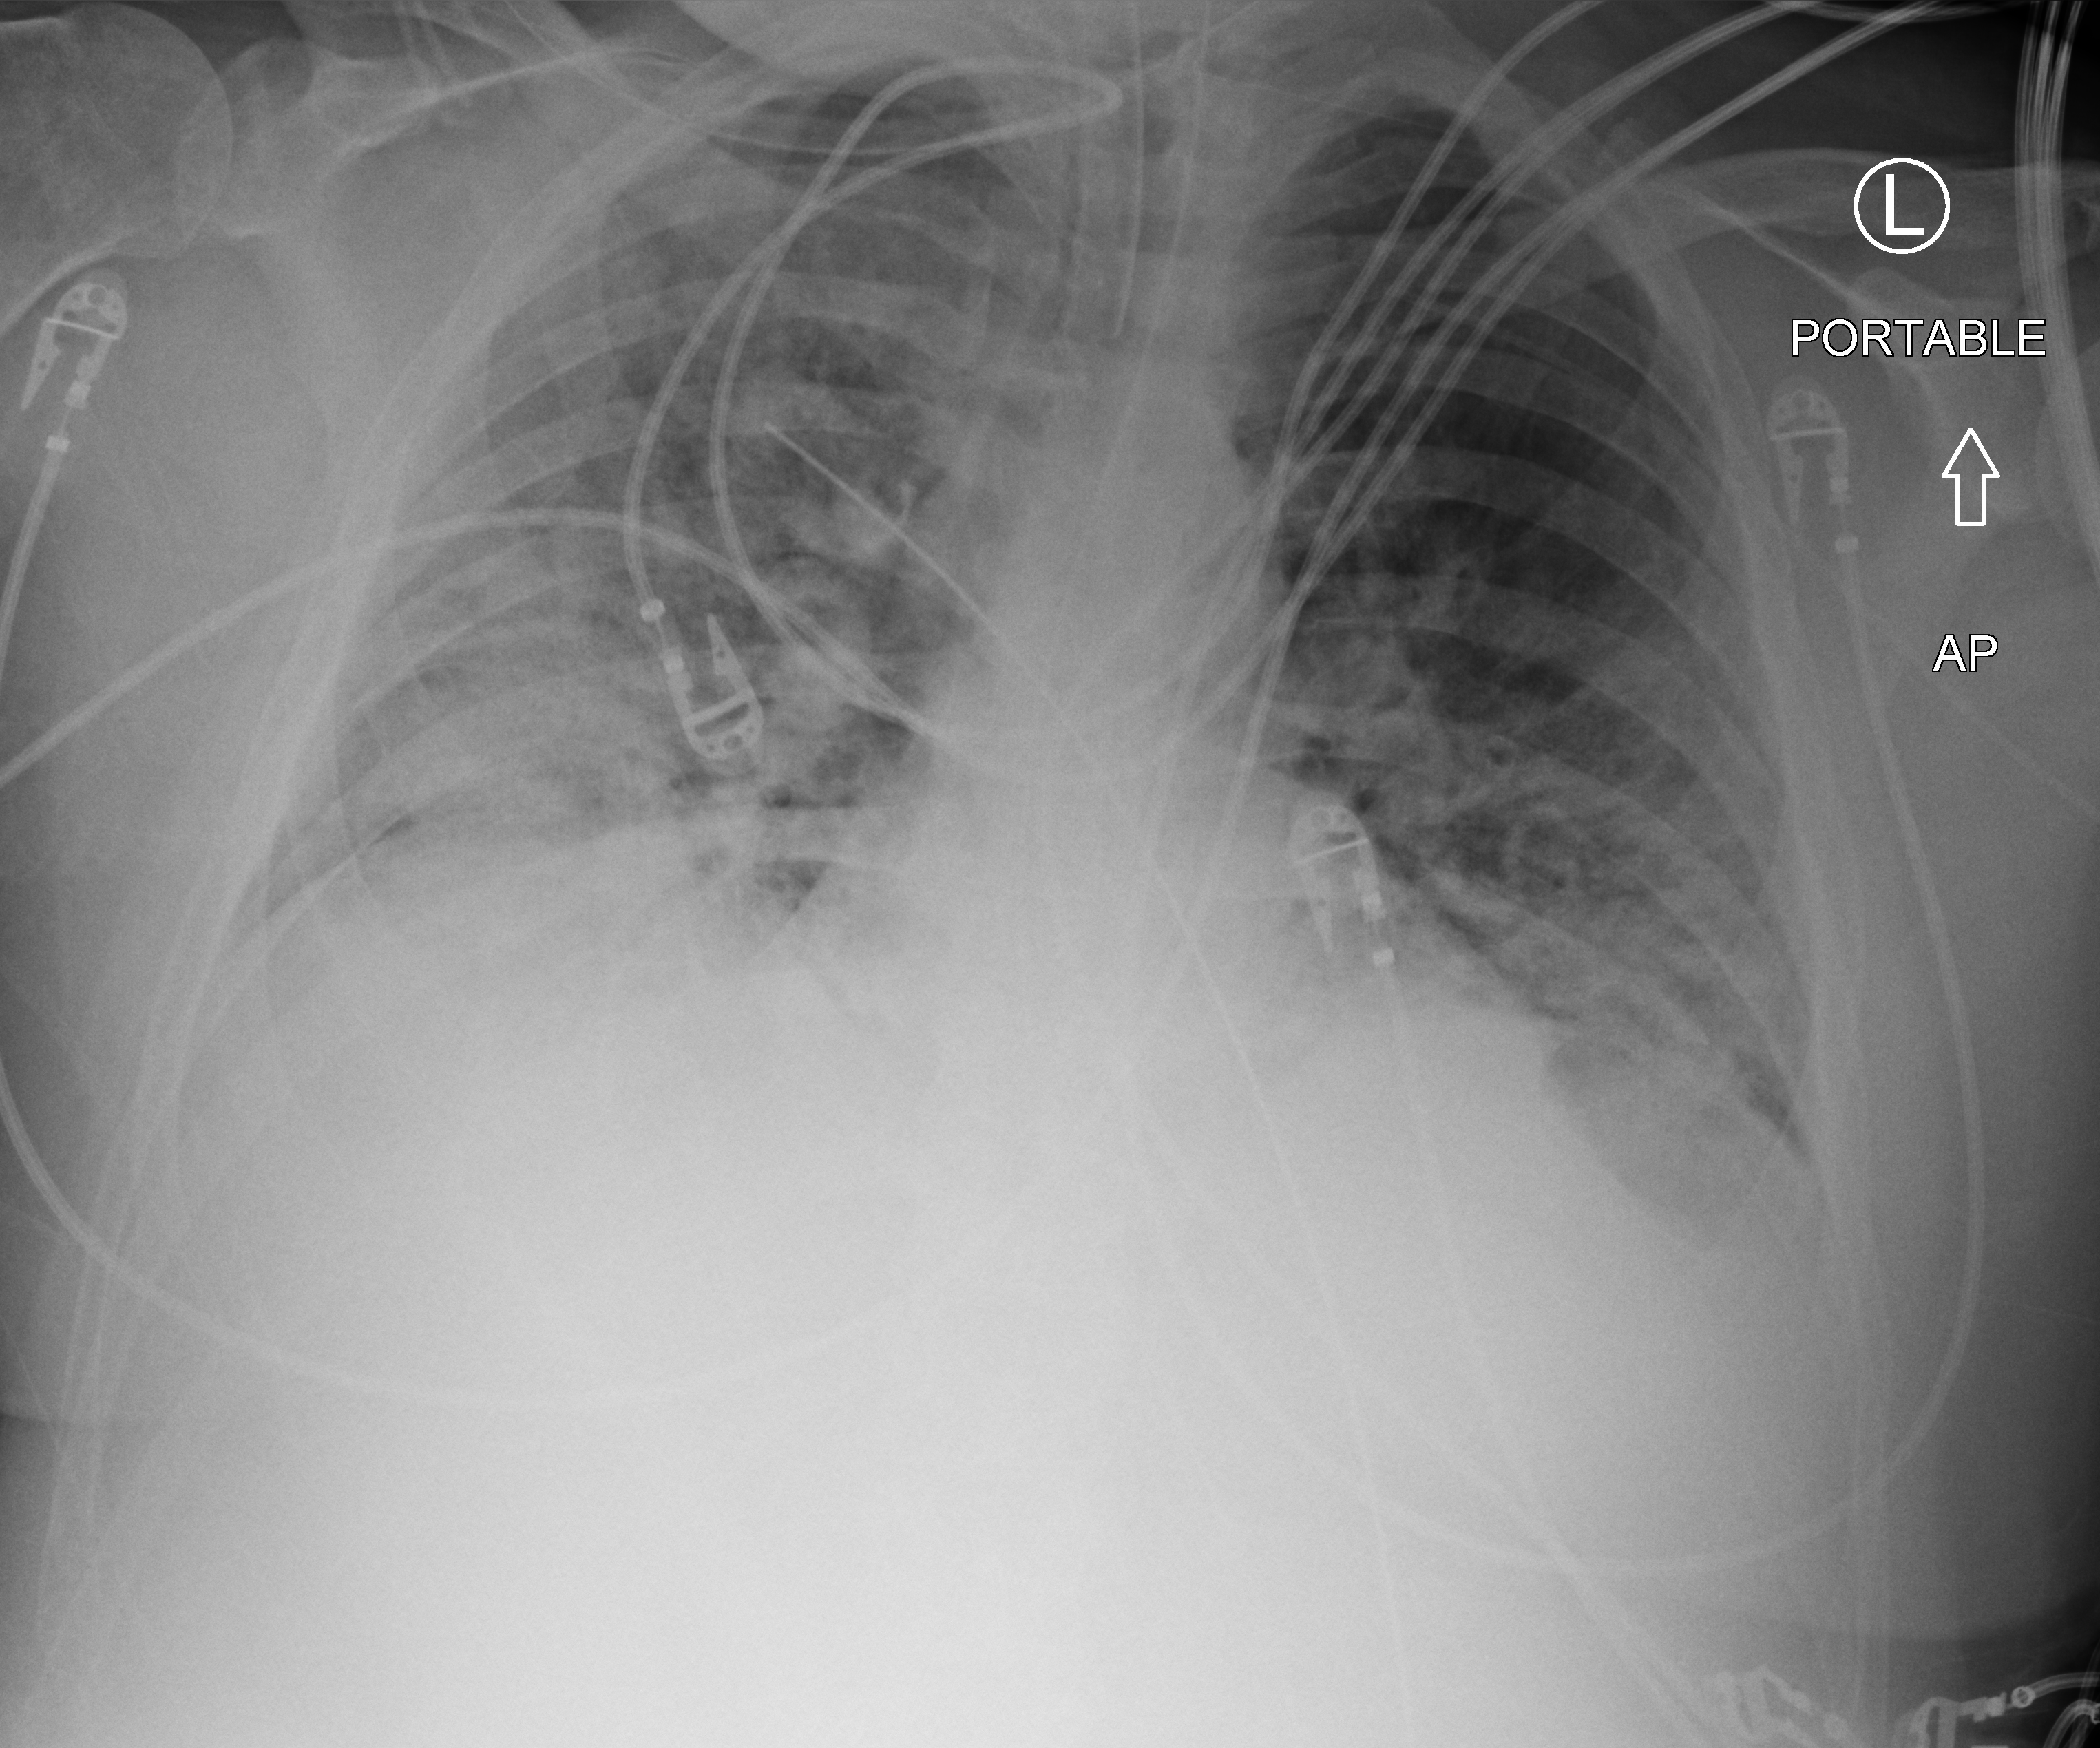
Bedside chest radiograph (computed radiography), anteroposterior (AP) projection. Male patient hospitalised with COVID-19, age 18–59 years.
From the hospital-stay record, not from the radiograph (when in the stay this image was taken is not recorded): mechanically ventilated during this hospital stay: yes; admitted to intensive care during this hospital stay: yes.